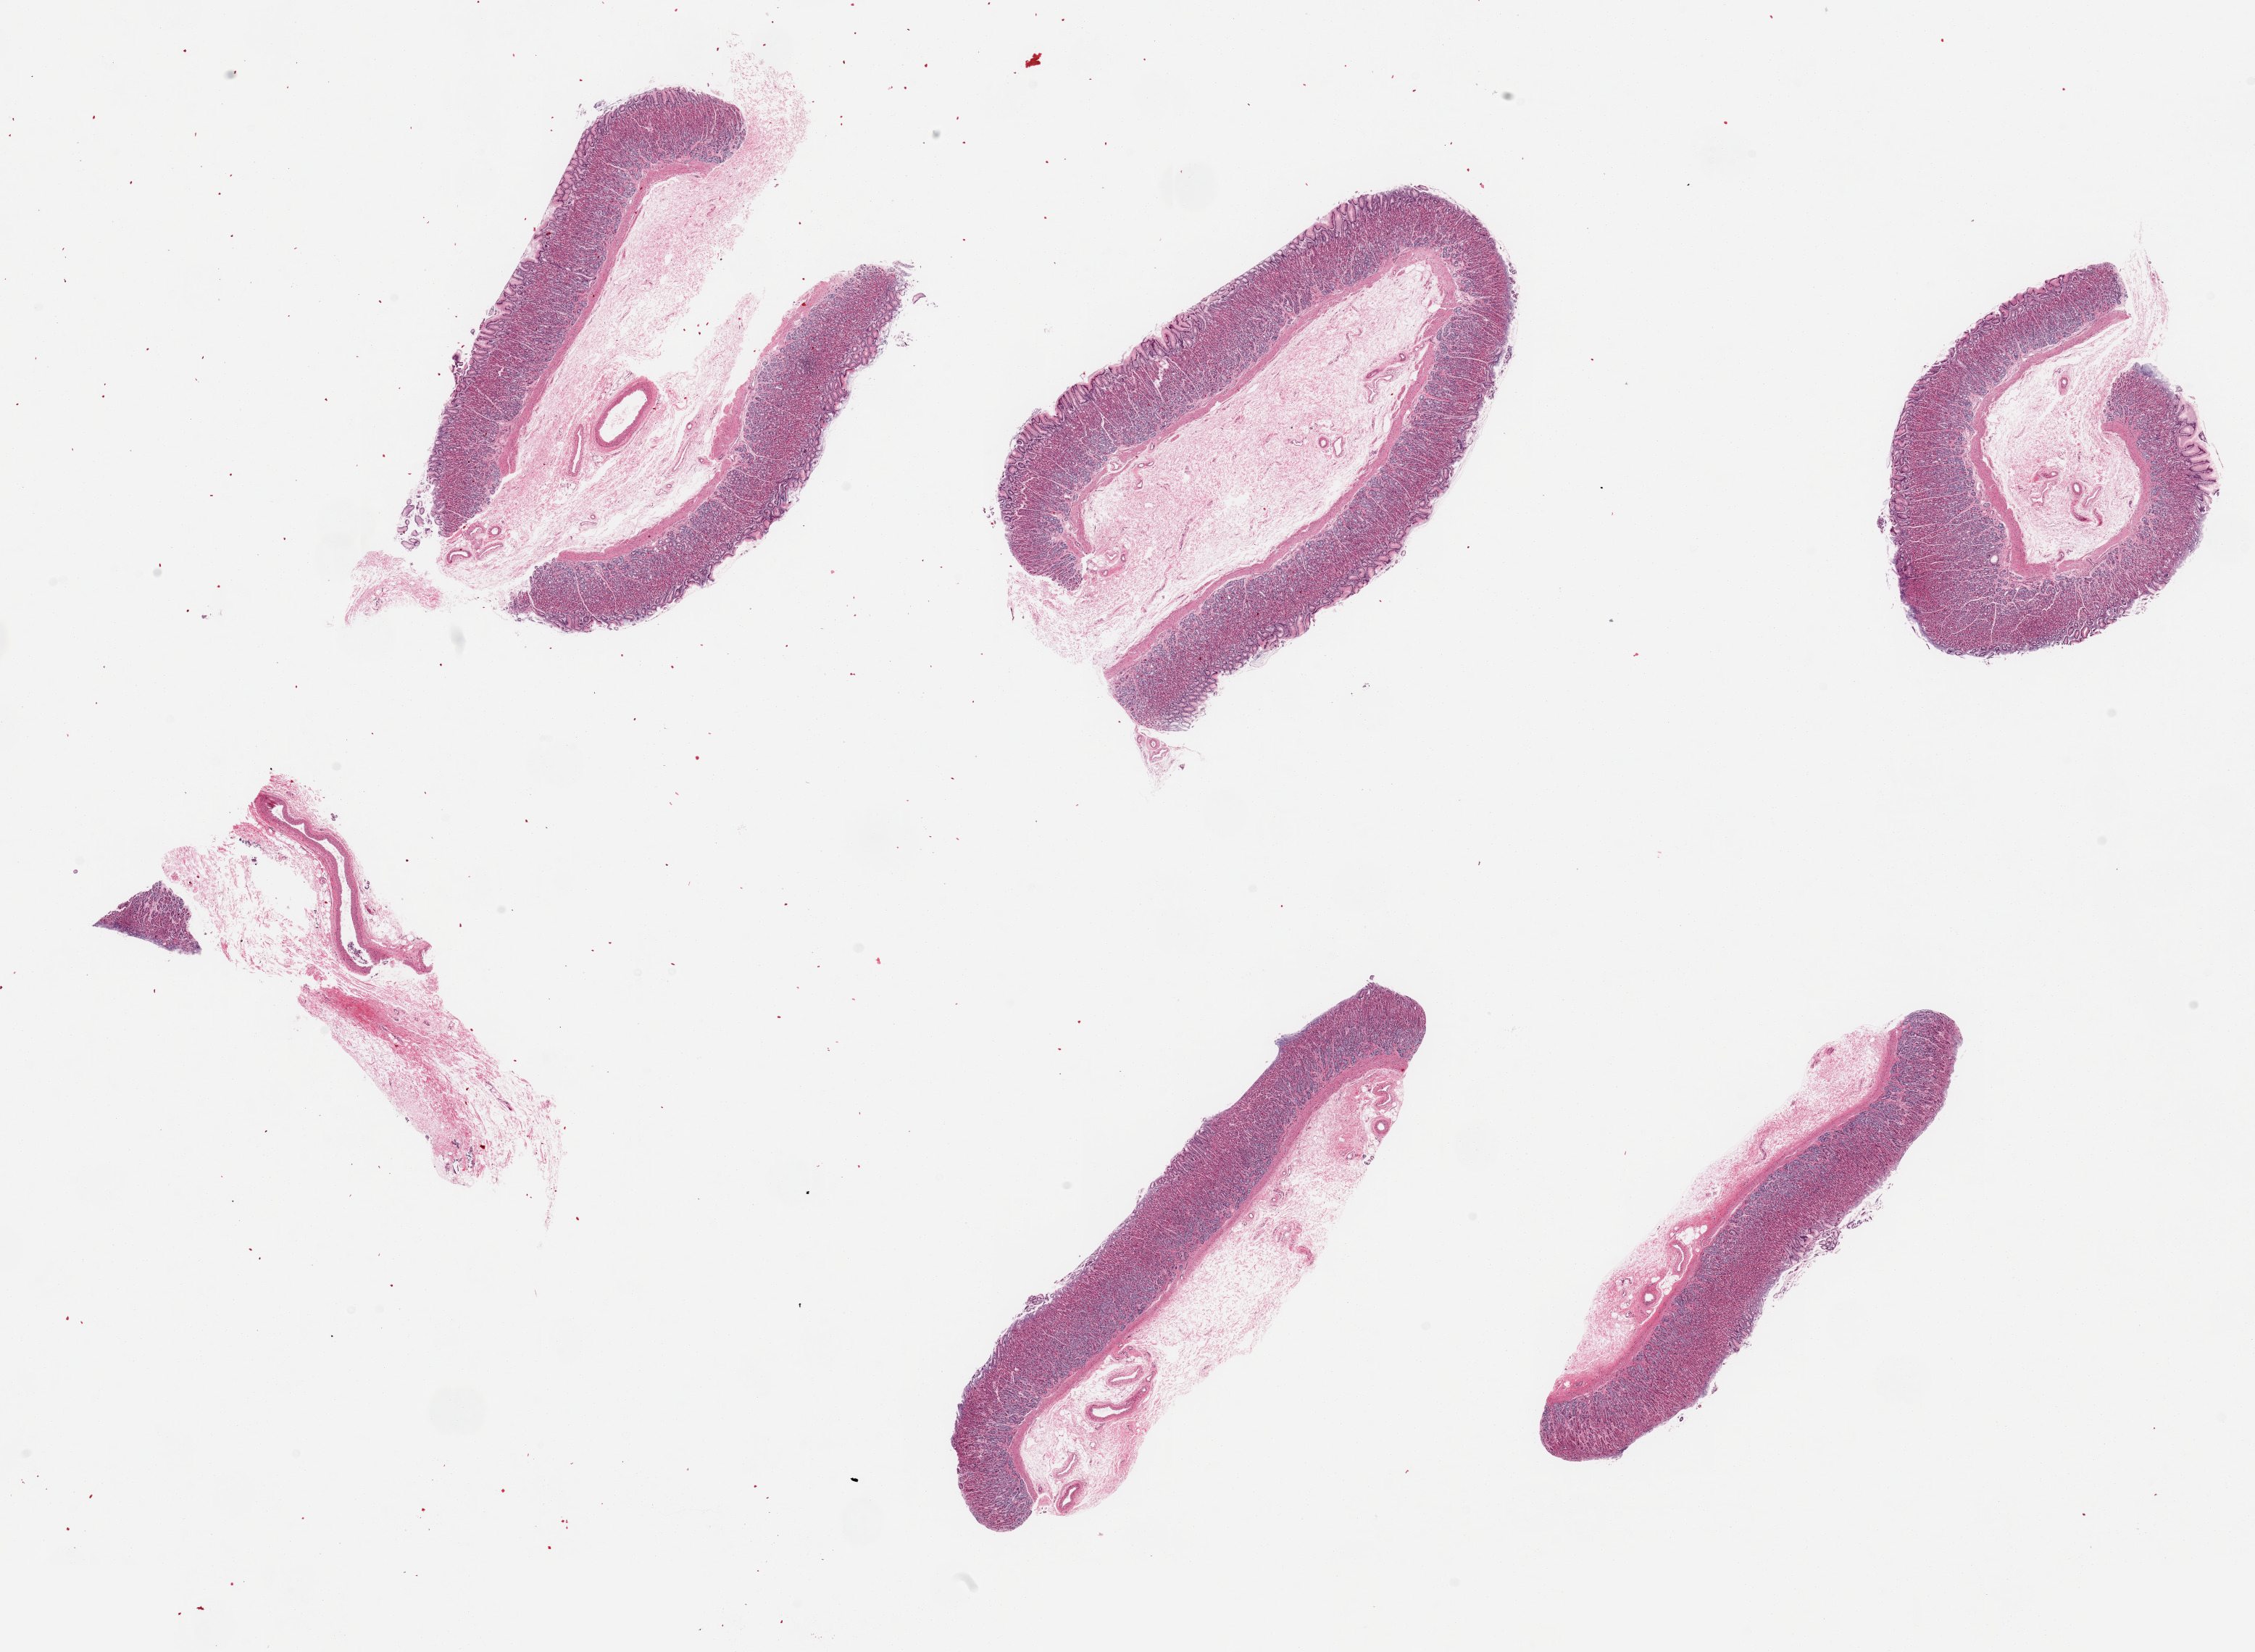
Digitized haematoxylin and eosin-stained section, brightfield — shown as a low-resolution overview of the whole scanned area (about 24.6 x 18.0 mm). Donor sex: female.
* specimen: PAXgene-fixed paraffin-embedded (PFPE) section; sampled site (target tissue): stomach; donor tissue sample